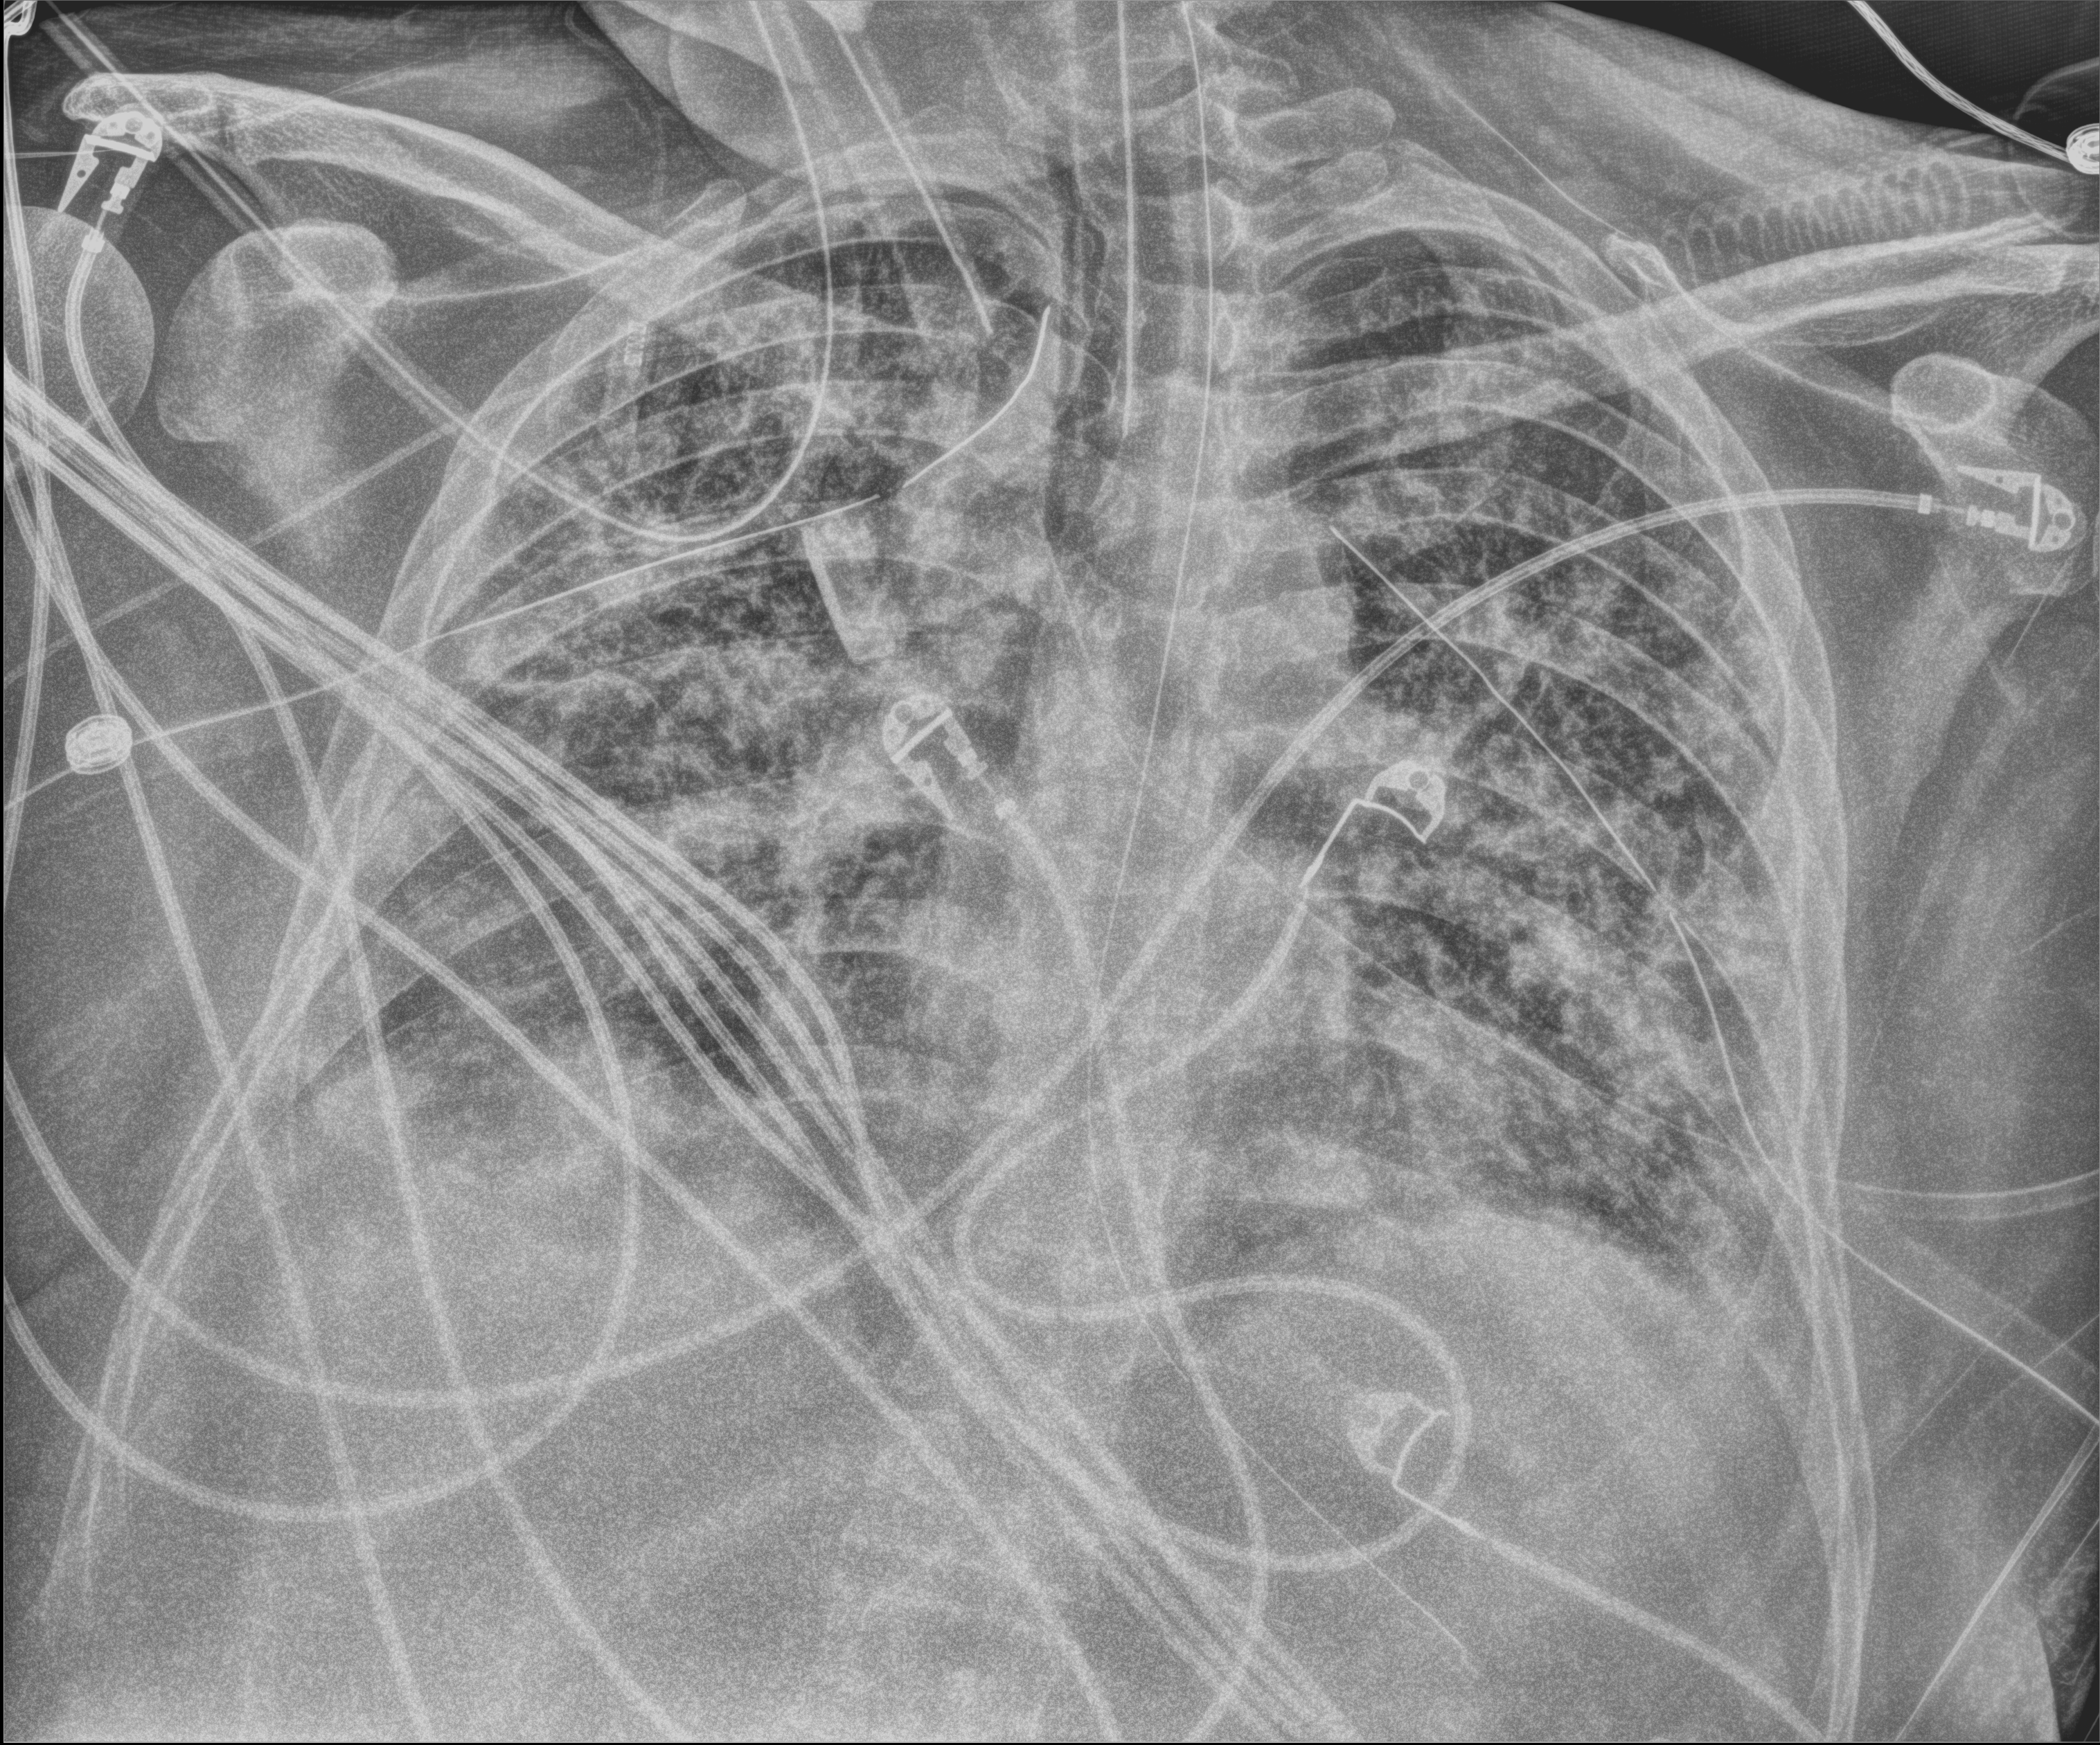
Portable chest radiograph, anteroposterior (AP) projection. Patient hospitalised with COVID-19; male, aged 18–59 years.
Admission-level facts for this patient (not findings on this image; timing relative to this image not recorded):
- other chronic lung disease (admission record): no
- length of hospital stay: 63 days
- admitted to intensive care during this hospital stay: yes